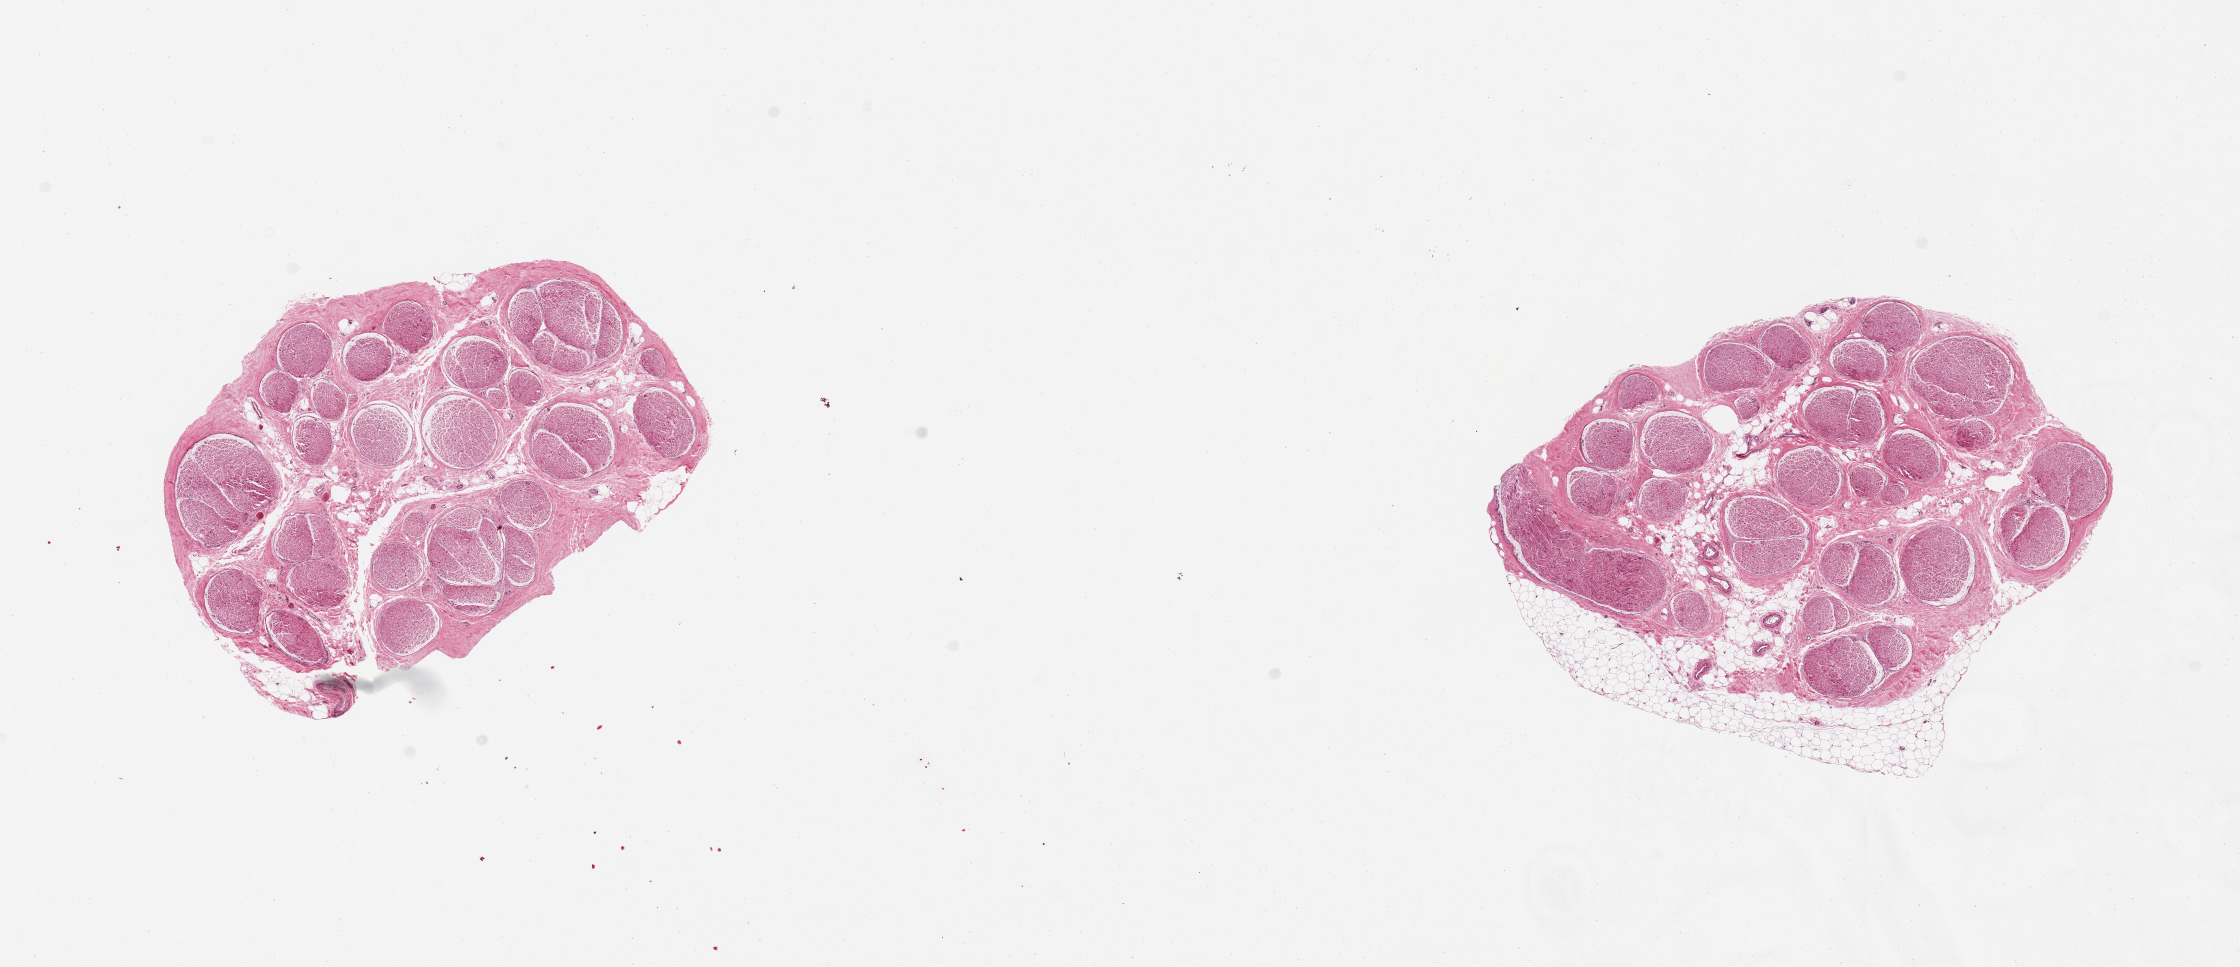
Digitized haematoxylin and eosin-stained section, a low-resolution overview of the entire scanned area, about 17.7 x 7.6 mm (slide scanned at 20x). PAXgene-fixed, paraffin-embedded tissue. Sampled site (target tissue): tibial nerve. Tissue donor sample. Donor sex: female.
Reviewer comment on this tissue sample: 2 pieces; 1 has 30% internal & external fat, other has 5%.